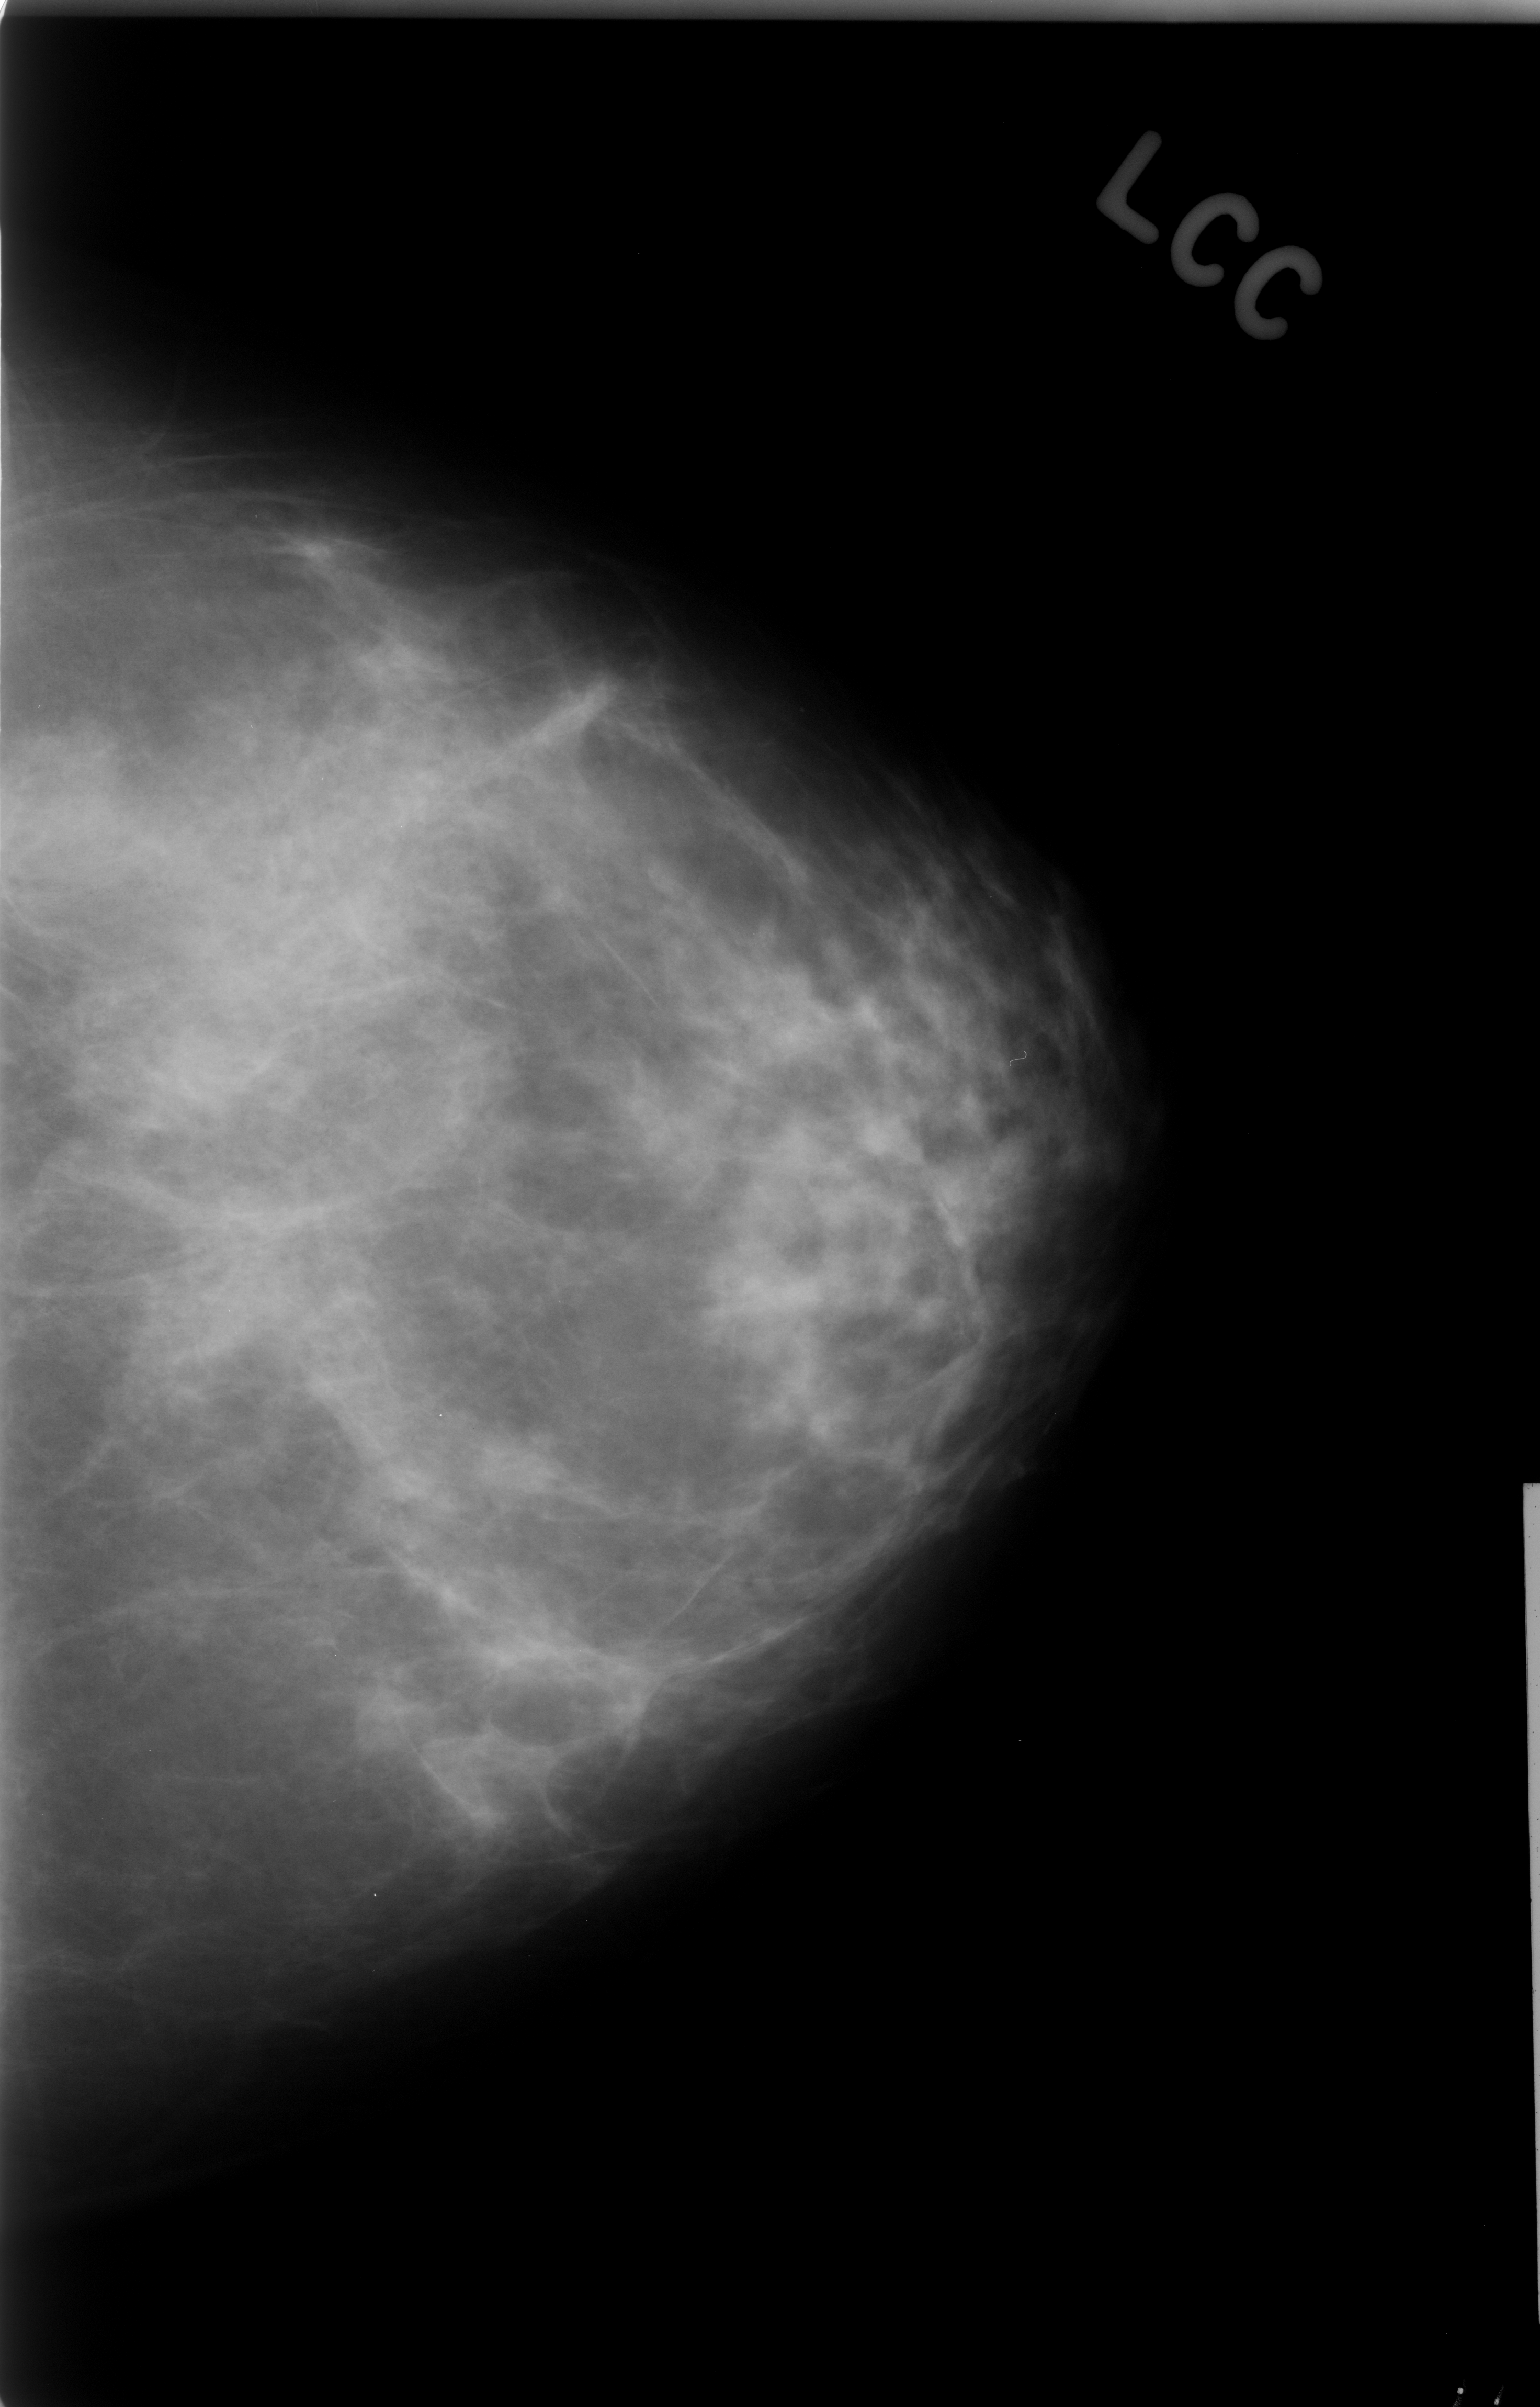
Mammogram (digitized film); left breast; CC view; BI-RADS breast density category 2 (scale 1–4); 1540 × 2407 image matrix.
Expert-marked regions of interest on this image (one box per marked abnormality):
- mass, shape asymmetric breast tissue; BI-RADS assessment category 3; subtlety rating 5 on a 1 (subtle) to 5 (obvious) scale; outcome (as recorded, no biopsy): benign without callback (not worked up further): bounding box [x1, y1, x2, y2] px = [116, 778, 434, 1088]